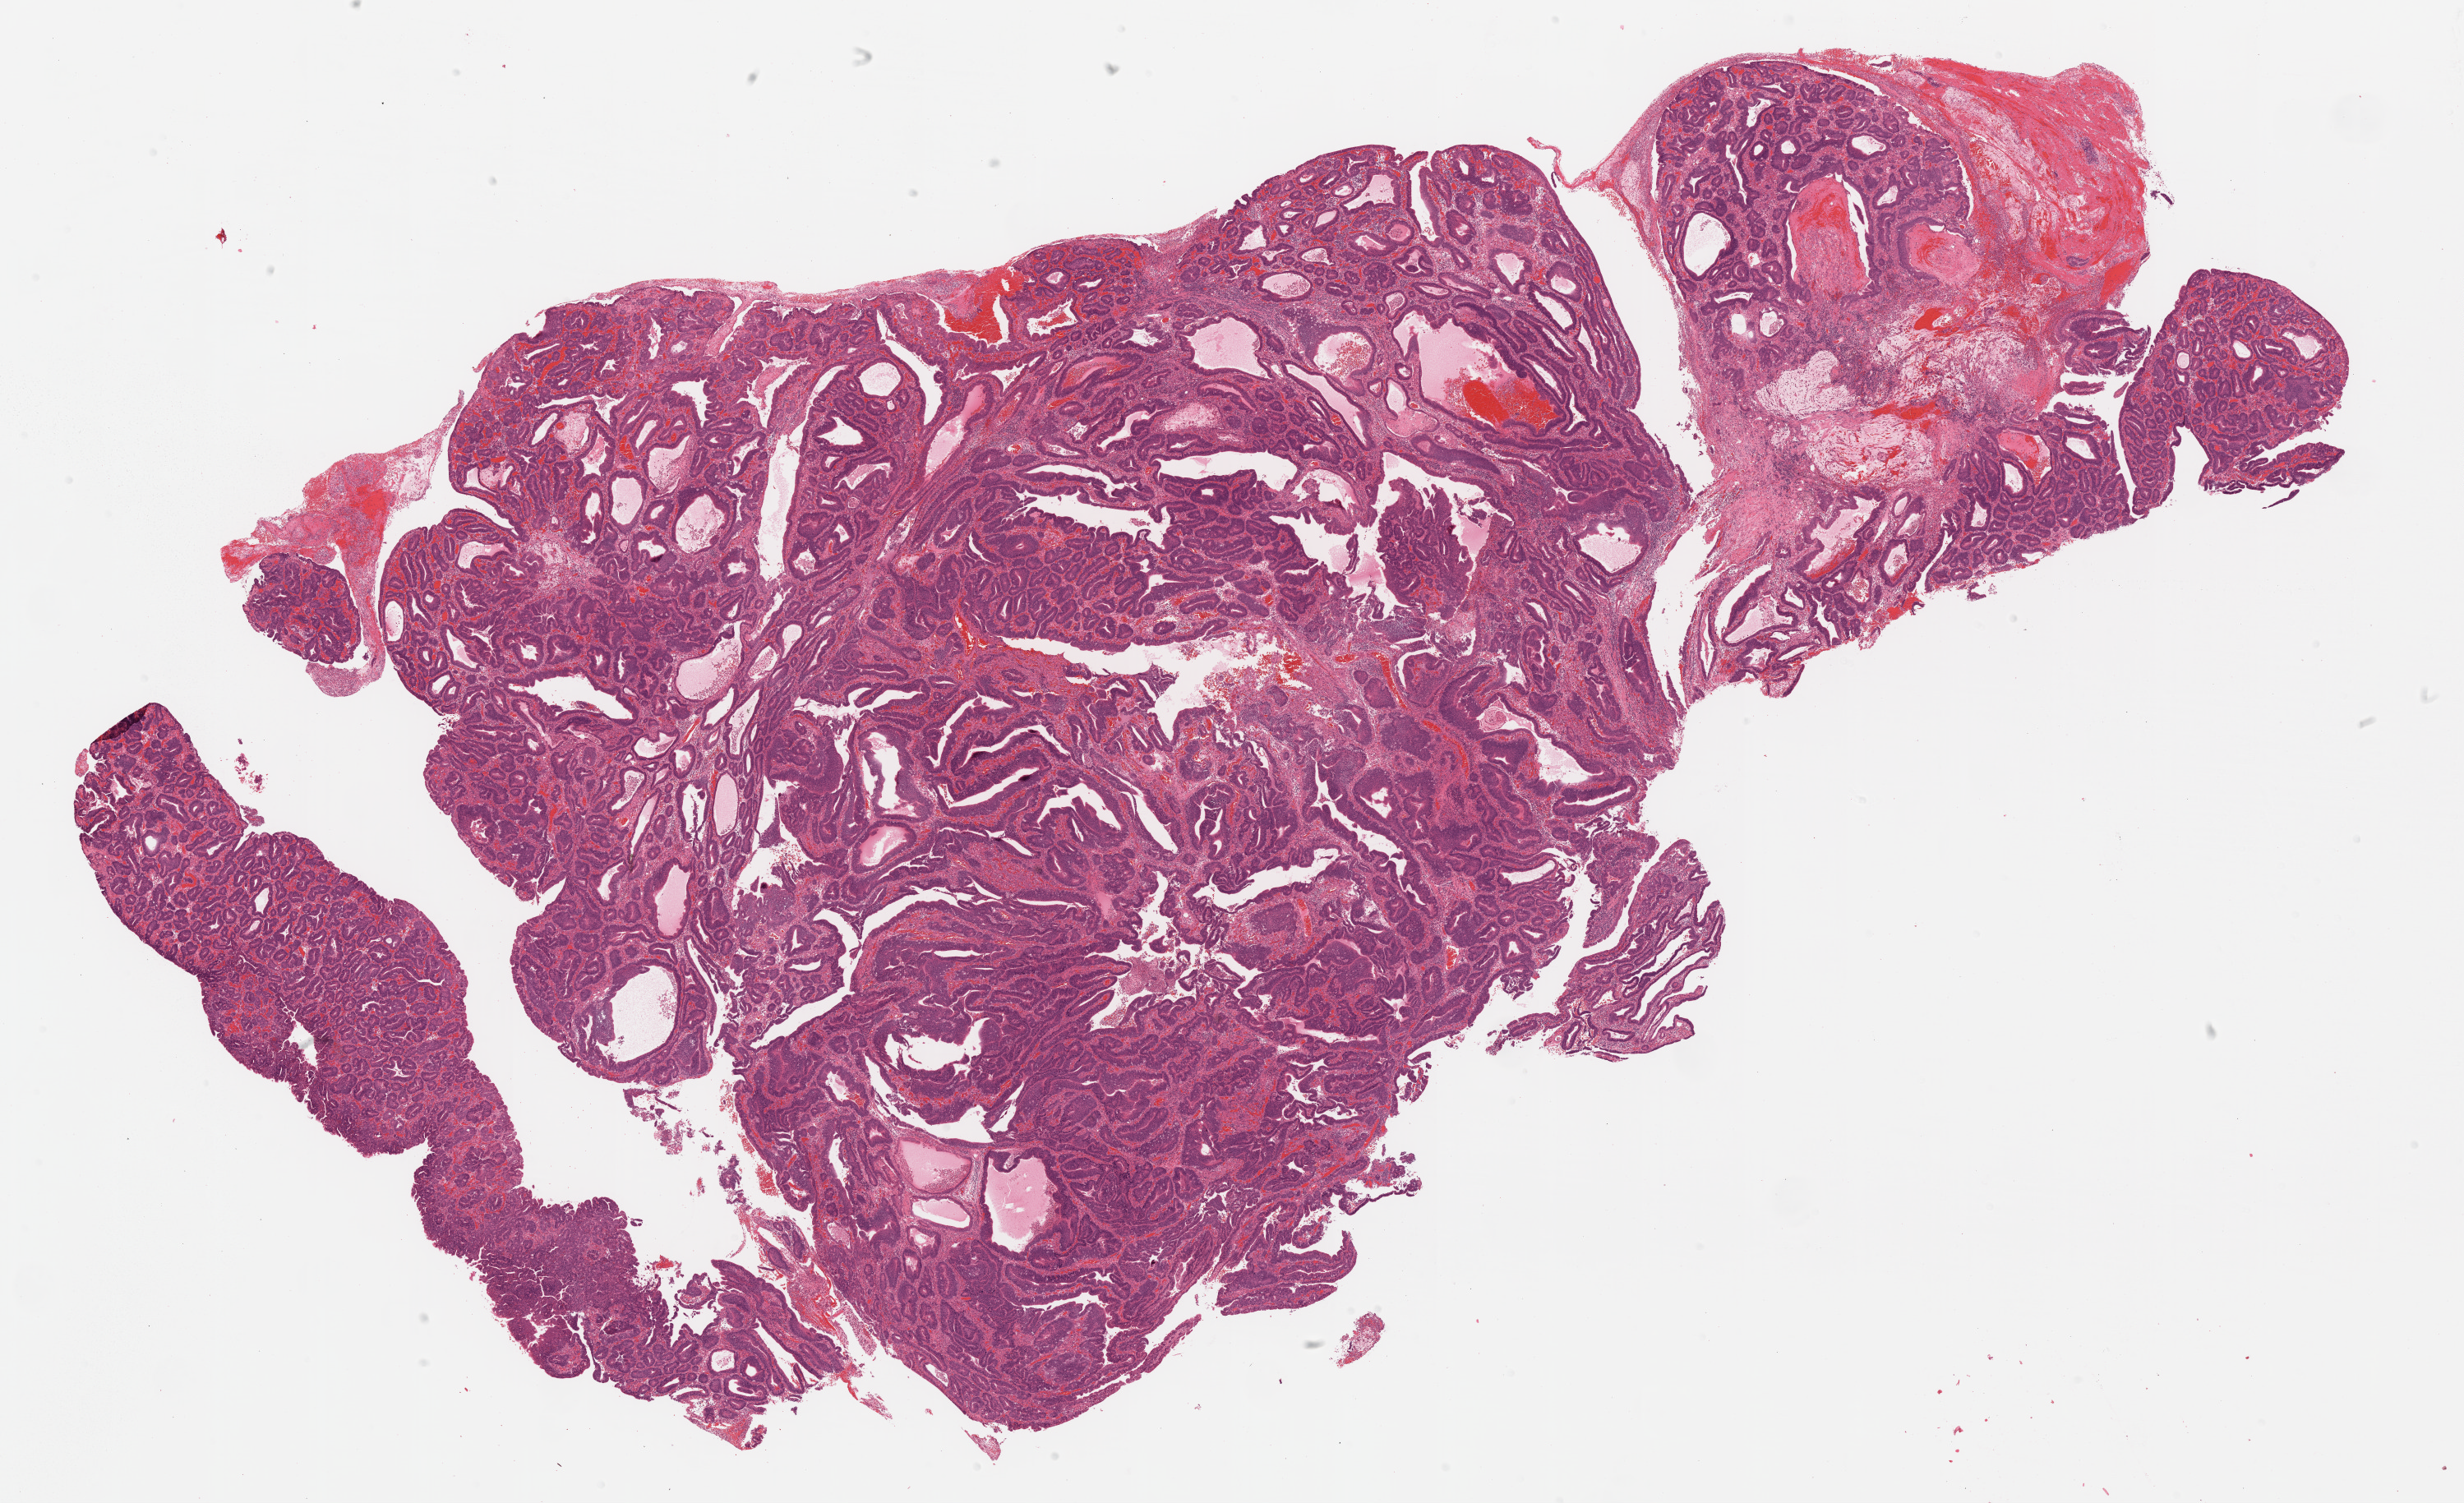
Digitized H&E tissue section (whole slide), shown as a low-resolution overview of the whole scanned area (about 24.0 x 14.6 mm); FFPE section; sample: primary tumour, stomach. Male patient. Histologic grade: G2 (moderately differentiated).
- pathologic diagnosis: Adenocarcinoma, intestinal type (body of stomach)
- AJCC pathologic stage: IA (6th edition)
- lymph nodes positive (case pathology): 0 of 25 examined